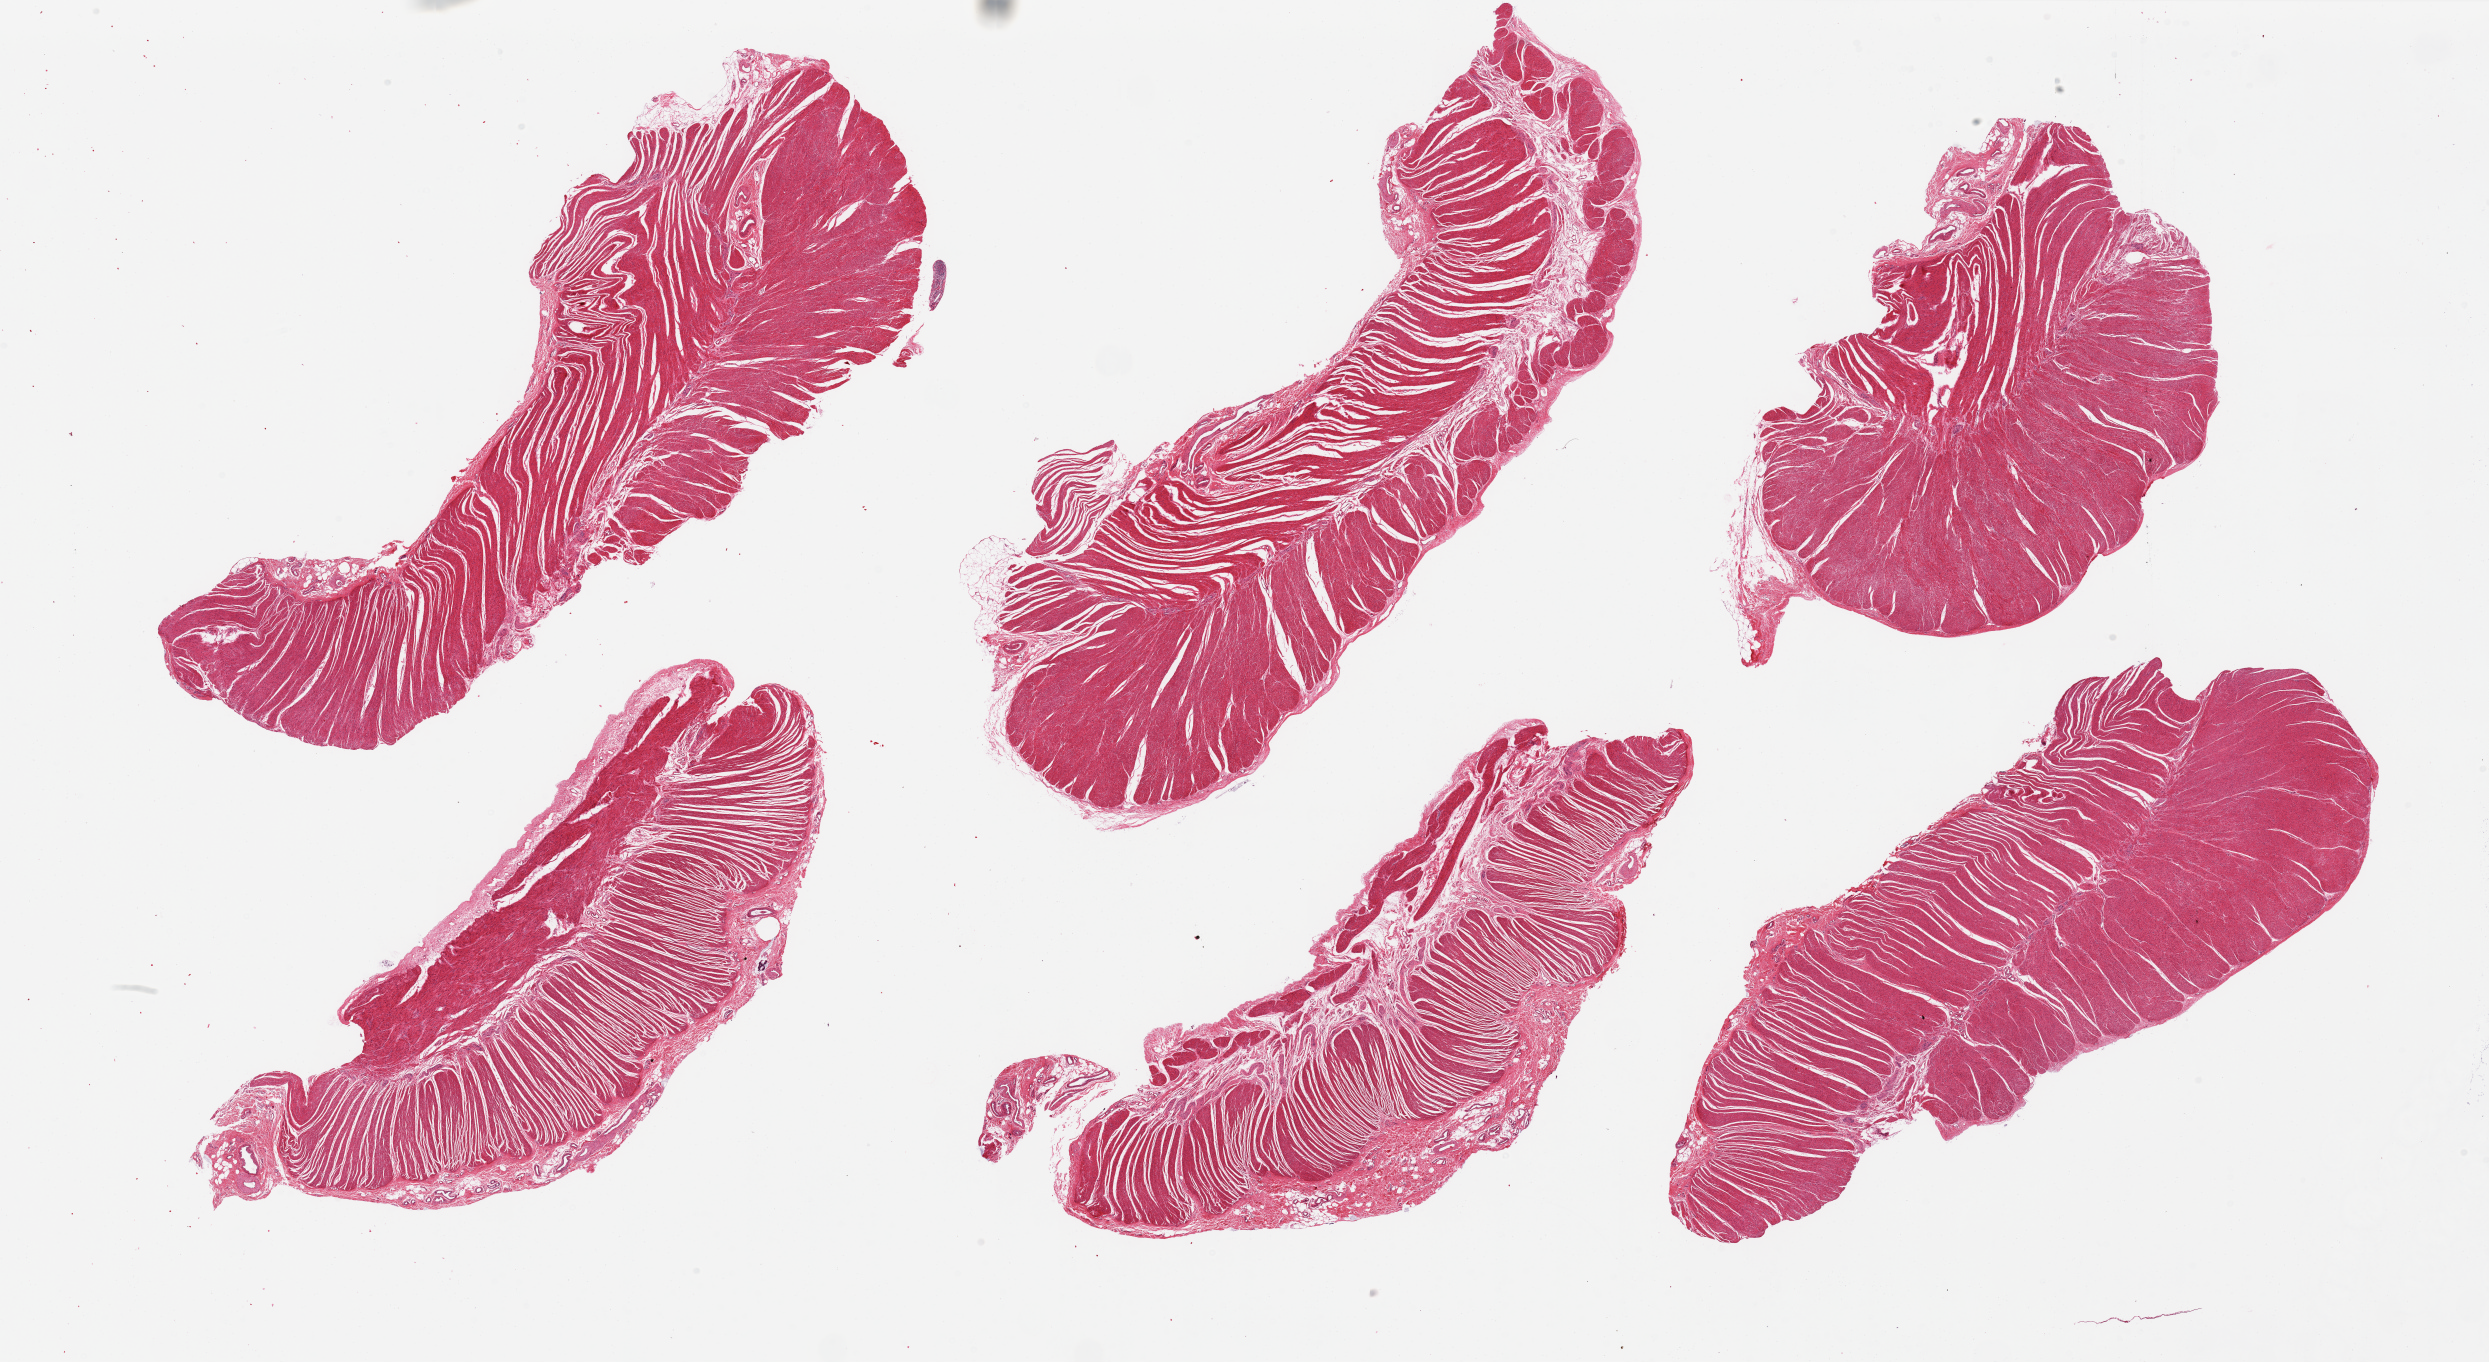
Digitized H&E-stained section, whole scanned area (about 39.4 x 21.5 mm, acquisition: 20x scan) shown as a low-resolution overview; PAXgene-fixed paraffin-embedded (PFPE) section; sampled site (target tissue): sigmoid colon; donor tissue sample. Female donor.
Pathologist's review note for this sample: 6 pieces, well trimmed.